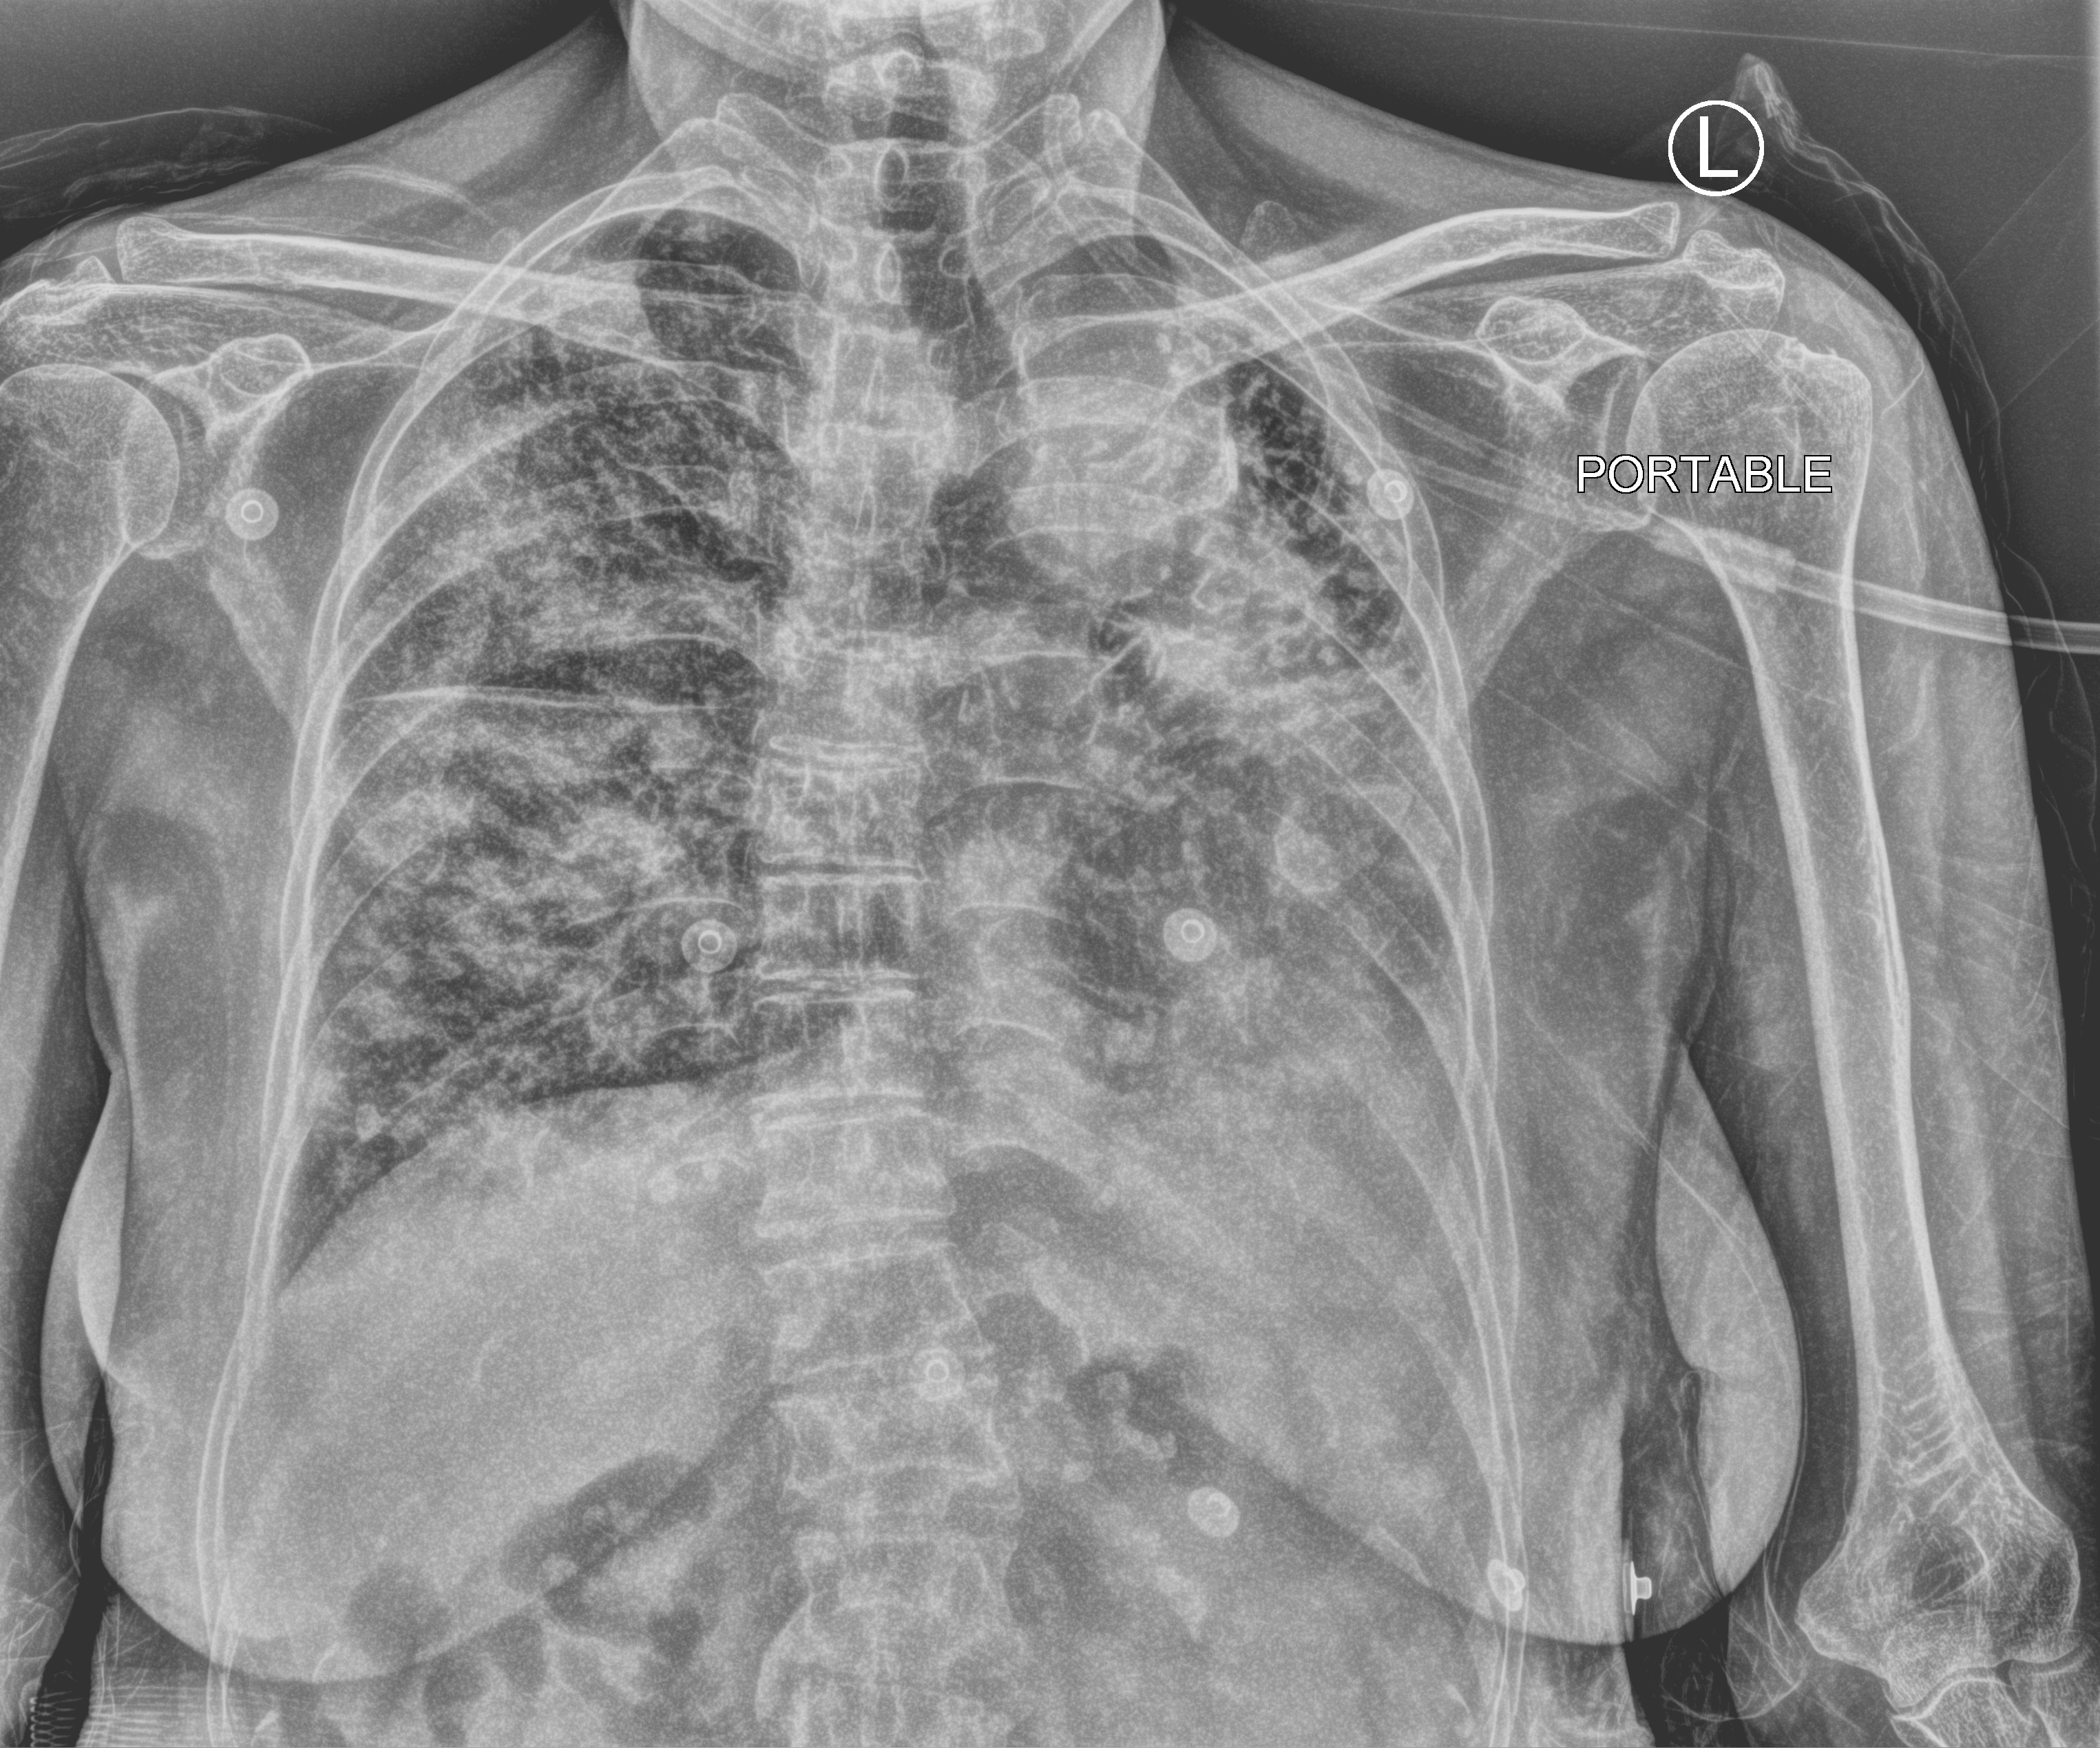
Portable chest radiograph. Female patient hospitalised with COVID-19, age 75–90 years.
From the hospital-stay record, not from the radiograph (when in the stay this image was taken is not recorded): admitted to intensive care during this hospital stay: no; mechanically ventilated during this hospital stay: no; hypertension (admission record): no.